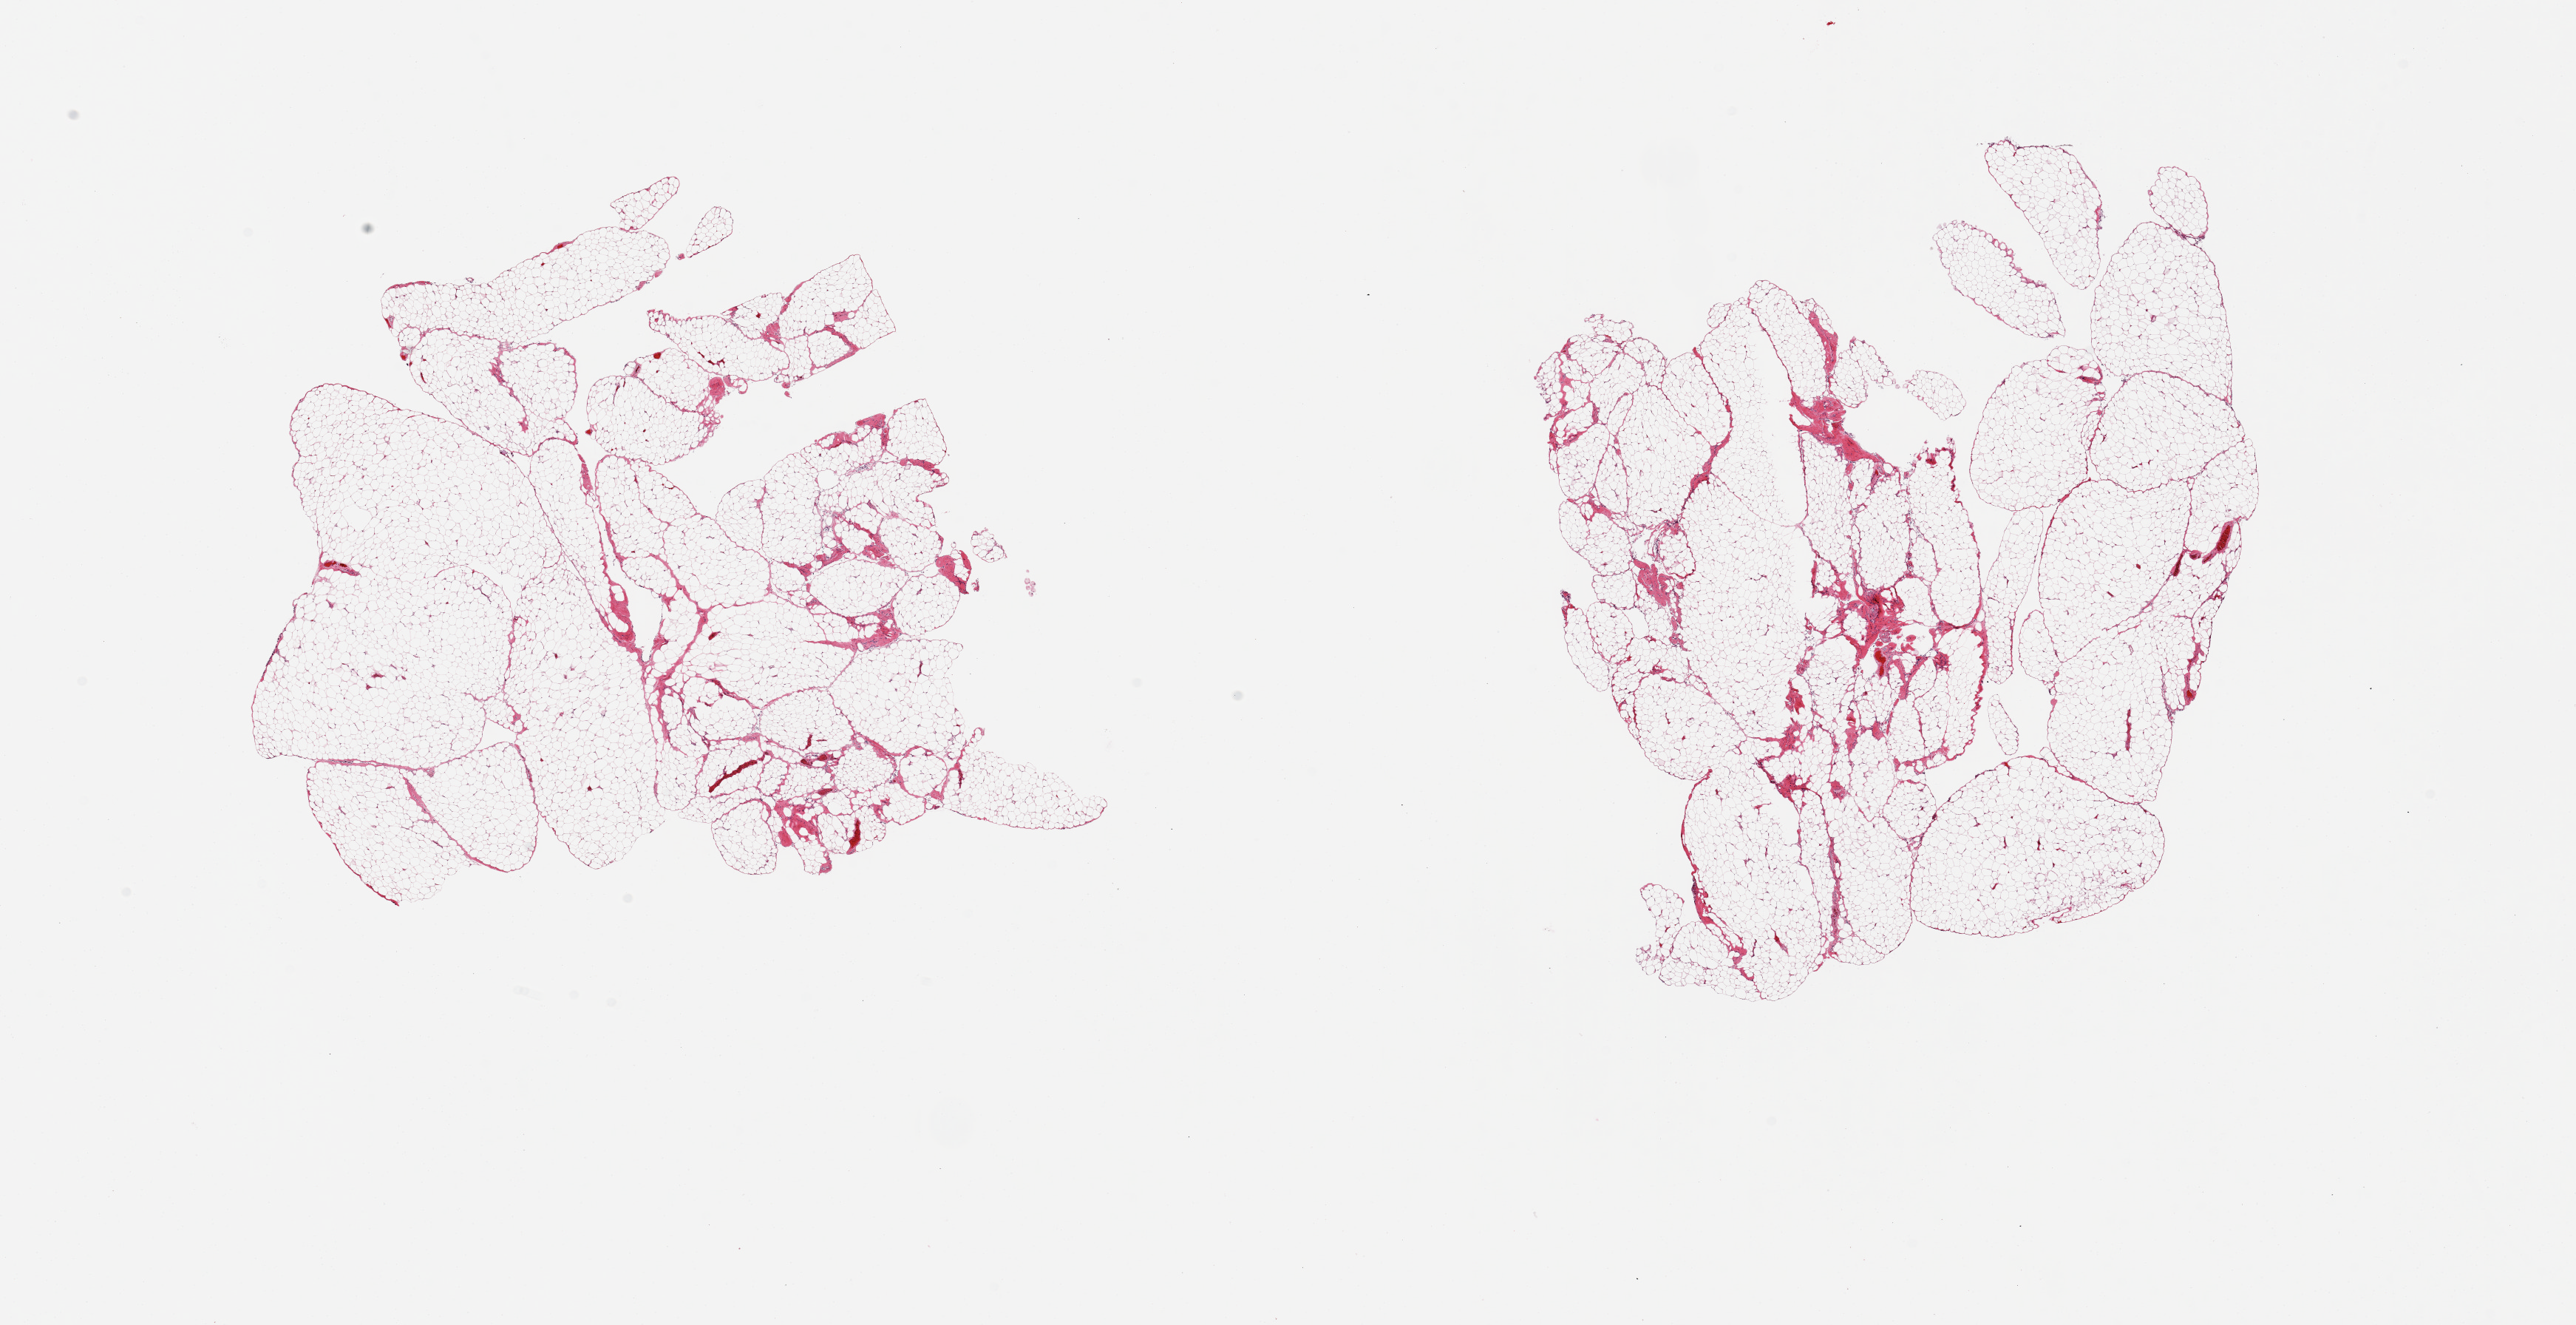
Whole-slide image, H&E stain, brightfield, whole scanned area (about 27.6 x 14.2 mm, acquisition: 20x scan) shown as a low-resolution overview. PAXgene-fixed paraffin-embedded (PFPE) section. Target tissue: omentum. Donor tissue sample. Donor sex: male.
Reviewer comment on this tissue sample: 2 pieces; less than 10% of fibrovascular component.